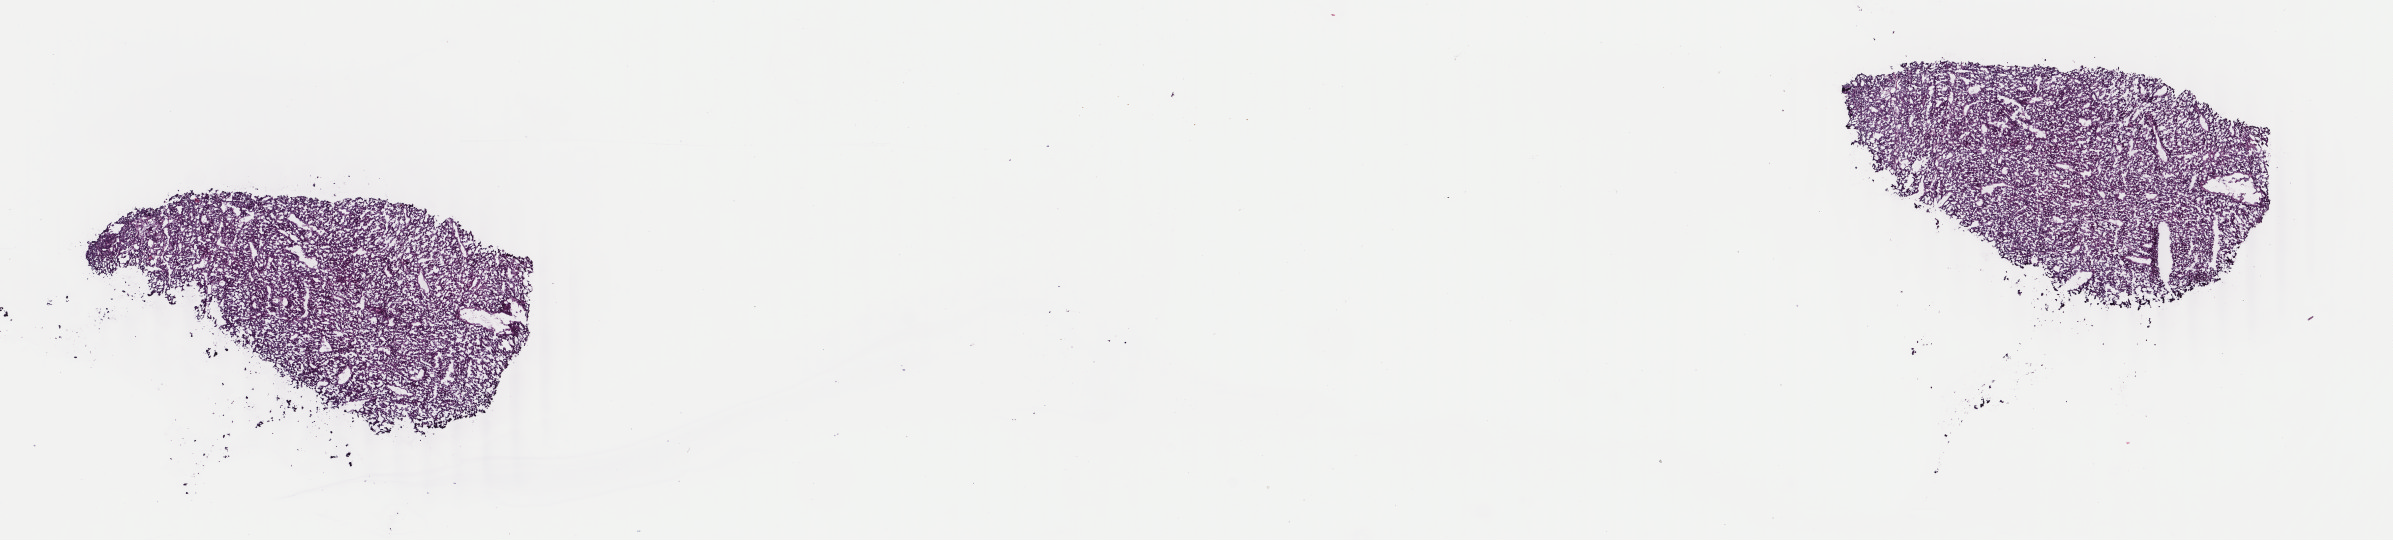
H&E whole-slide image, shown as a low-resolution overview of the whole scanned area (about 19.0 x 4.3 mm); frozen section from the top of the tissue portion; sample: primary tumour, adrenal cortex. Male, age 30 years at initial diagnosis. Slide review estimates, as recorded: tumour cells 100%, tumour nuclei 80%, normal cells 0%, stromal cells 0%, necrosis 0%. Infiltration values recorded for this section: lymphocyte infiltration 2%, monocyte infiltration 0%, neutrophil infiltration 0%.
Laterality: right. Pathologic diagnosis: Adrenal cortical carcinoma (cortex of adrenal gland).